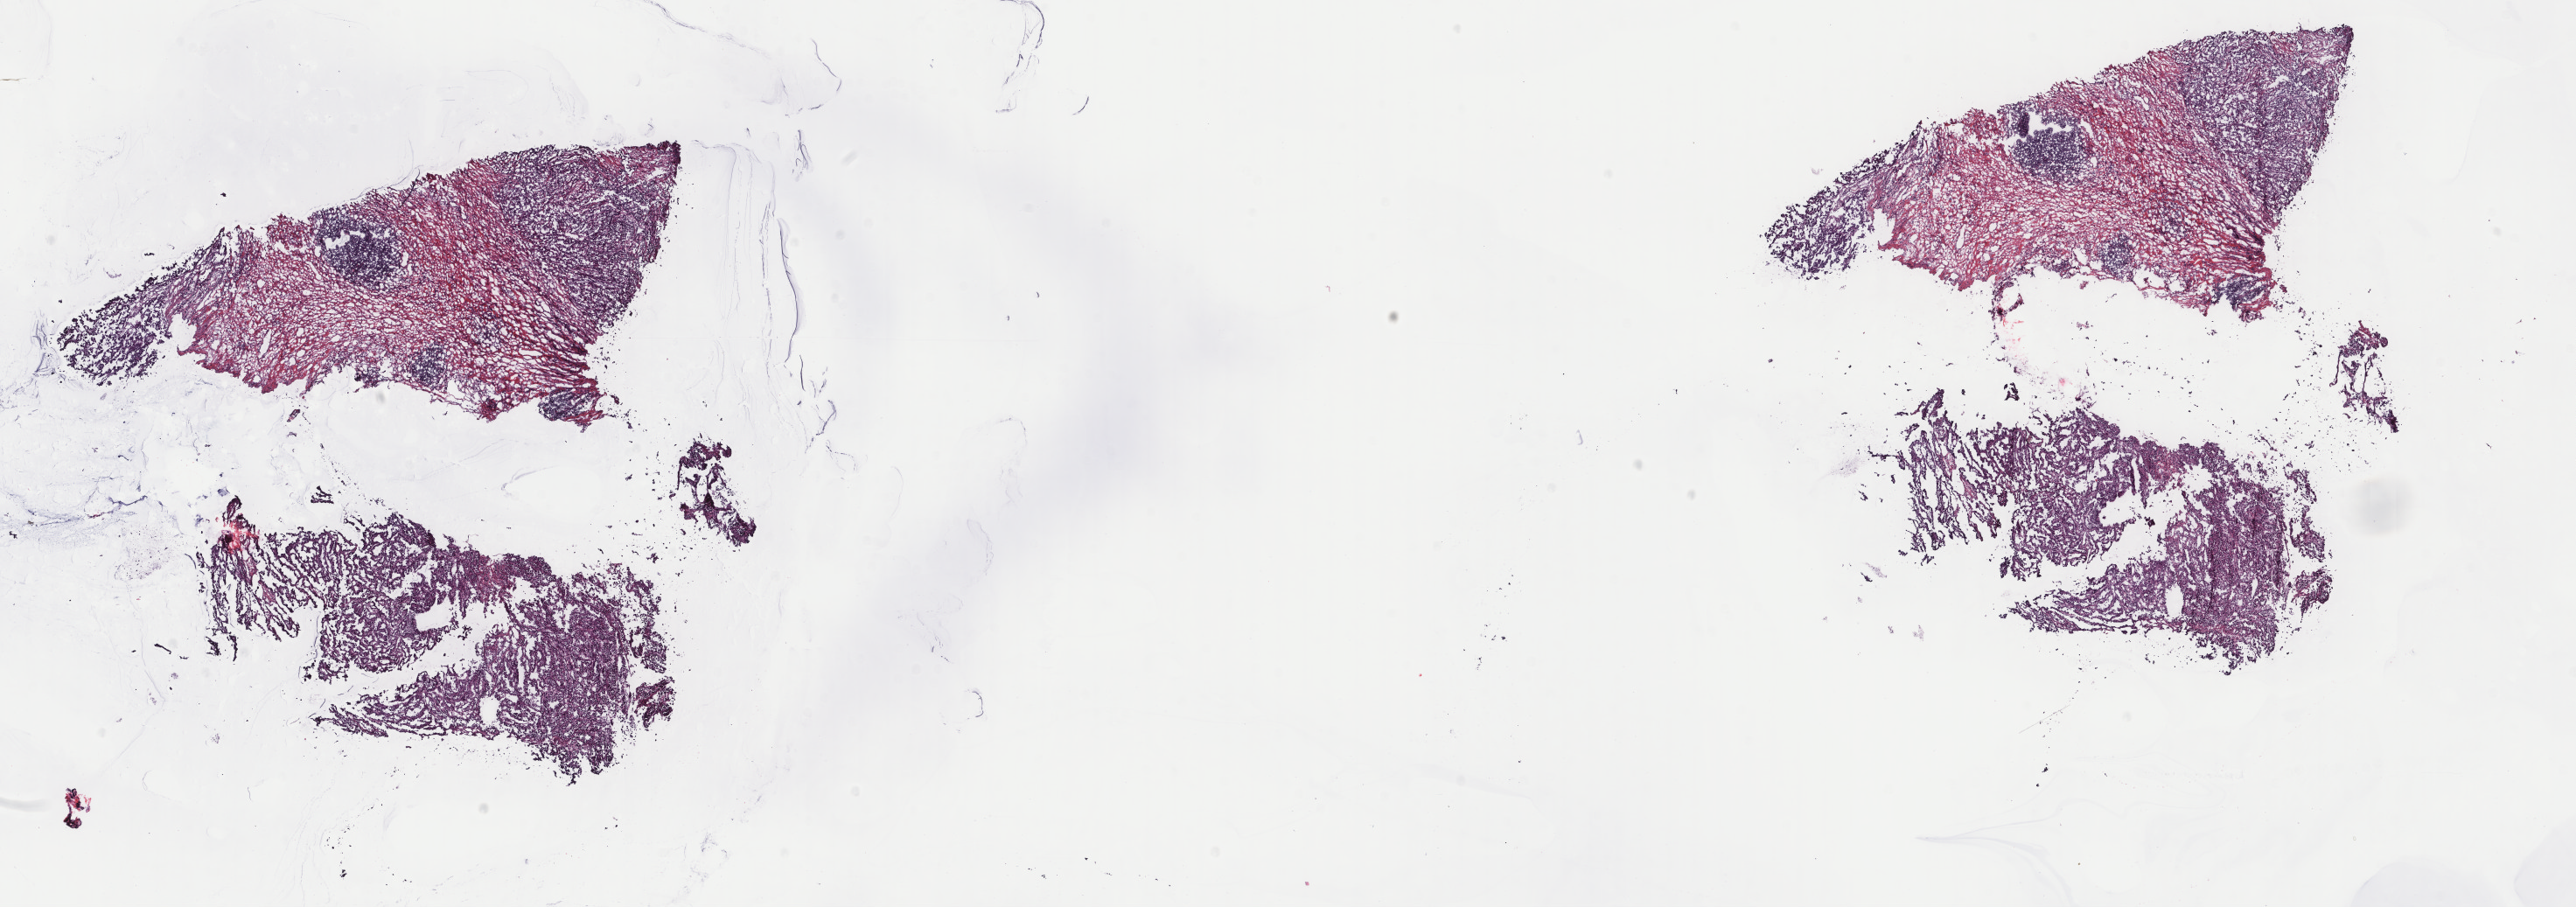
H&E-stained whole-slide image, a low-resolution overview of the entire scanned area, about 23.4 x 8.2 mm (from a 40x scan); frozen section from the top of the tissue portion; kidney, primary tumour sample. Patient: female, age at initial diagnosis 54 years. Slide review estimates, as recorded: tumour cells 100%, tumour nuclei 80%, normal cells 0%, stromal cells 0%, necrosis 0%. Infiltration values recorded for this section: lymphocyte infiltration 1%, monocyte infiltration 0%, neutrophil infiltration 0%.
AJCC pathologic stage: III. Laterality: left. Lymph nodes positive (case pathology): 1 of 5 examined. Histologic diagnosis: Papillary adenocarcinoma, NOS. TNM: T3a N1 MX.